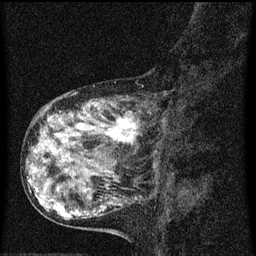
Breast MRI (dynamic contrast-enhanced), one sagittal slice. Position 22 of 60 along the scan axis. Dynamic contrast-enhanced series, image 2 of 3 at this slice position (ordered by acquisition). 1.5 T. TE 4.2 ms, TR 8 ms. 2 mm slice thickness. 256 × 256 image matrix. Female patient, age 55 years.
Structures marked on this image (semi-automatically segmented with operator editing):
- analysis volume of interest (the breast-tissue region the enhancement analysis was run in; not a lesion): bounding box (x1, y1, x2, y2) in pixels: (38, 92, 173, 159)
- tumour enhancement mask (voxels above the 70 % enhancement threshold inside the analysis volume of interest): (94, 116, 141, 145)